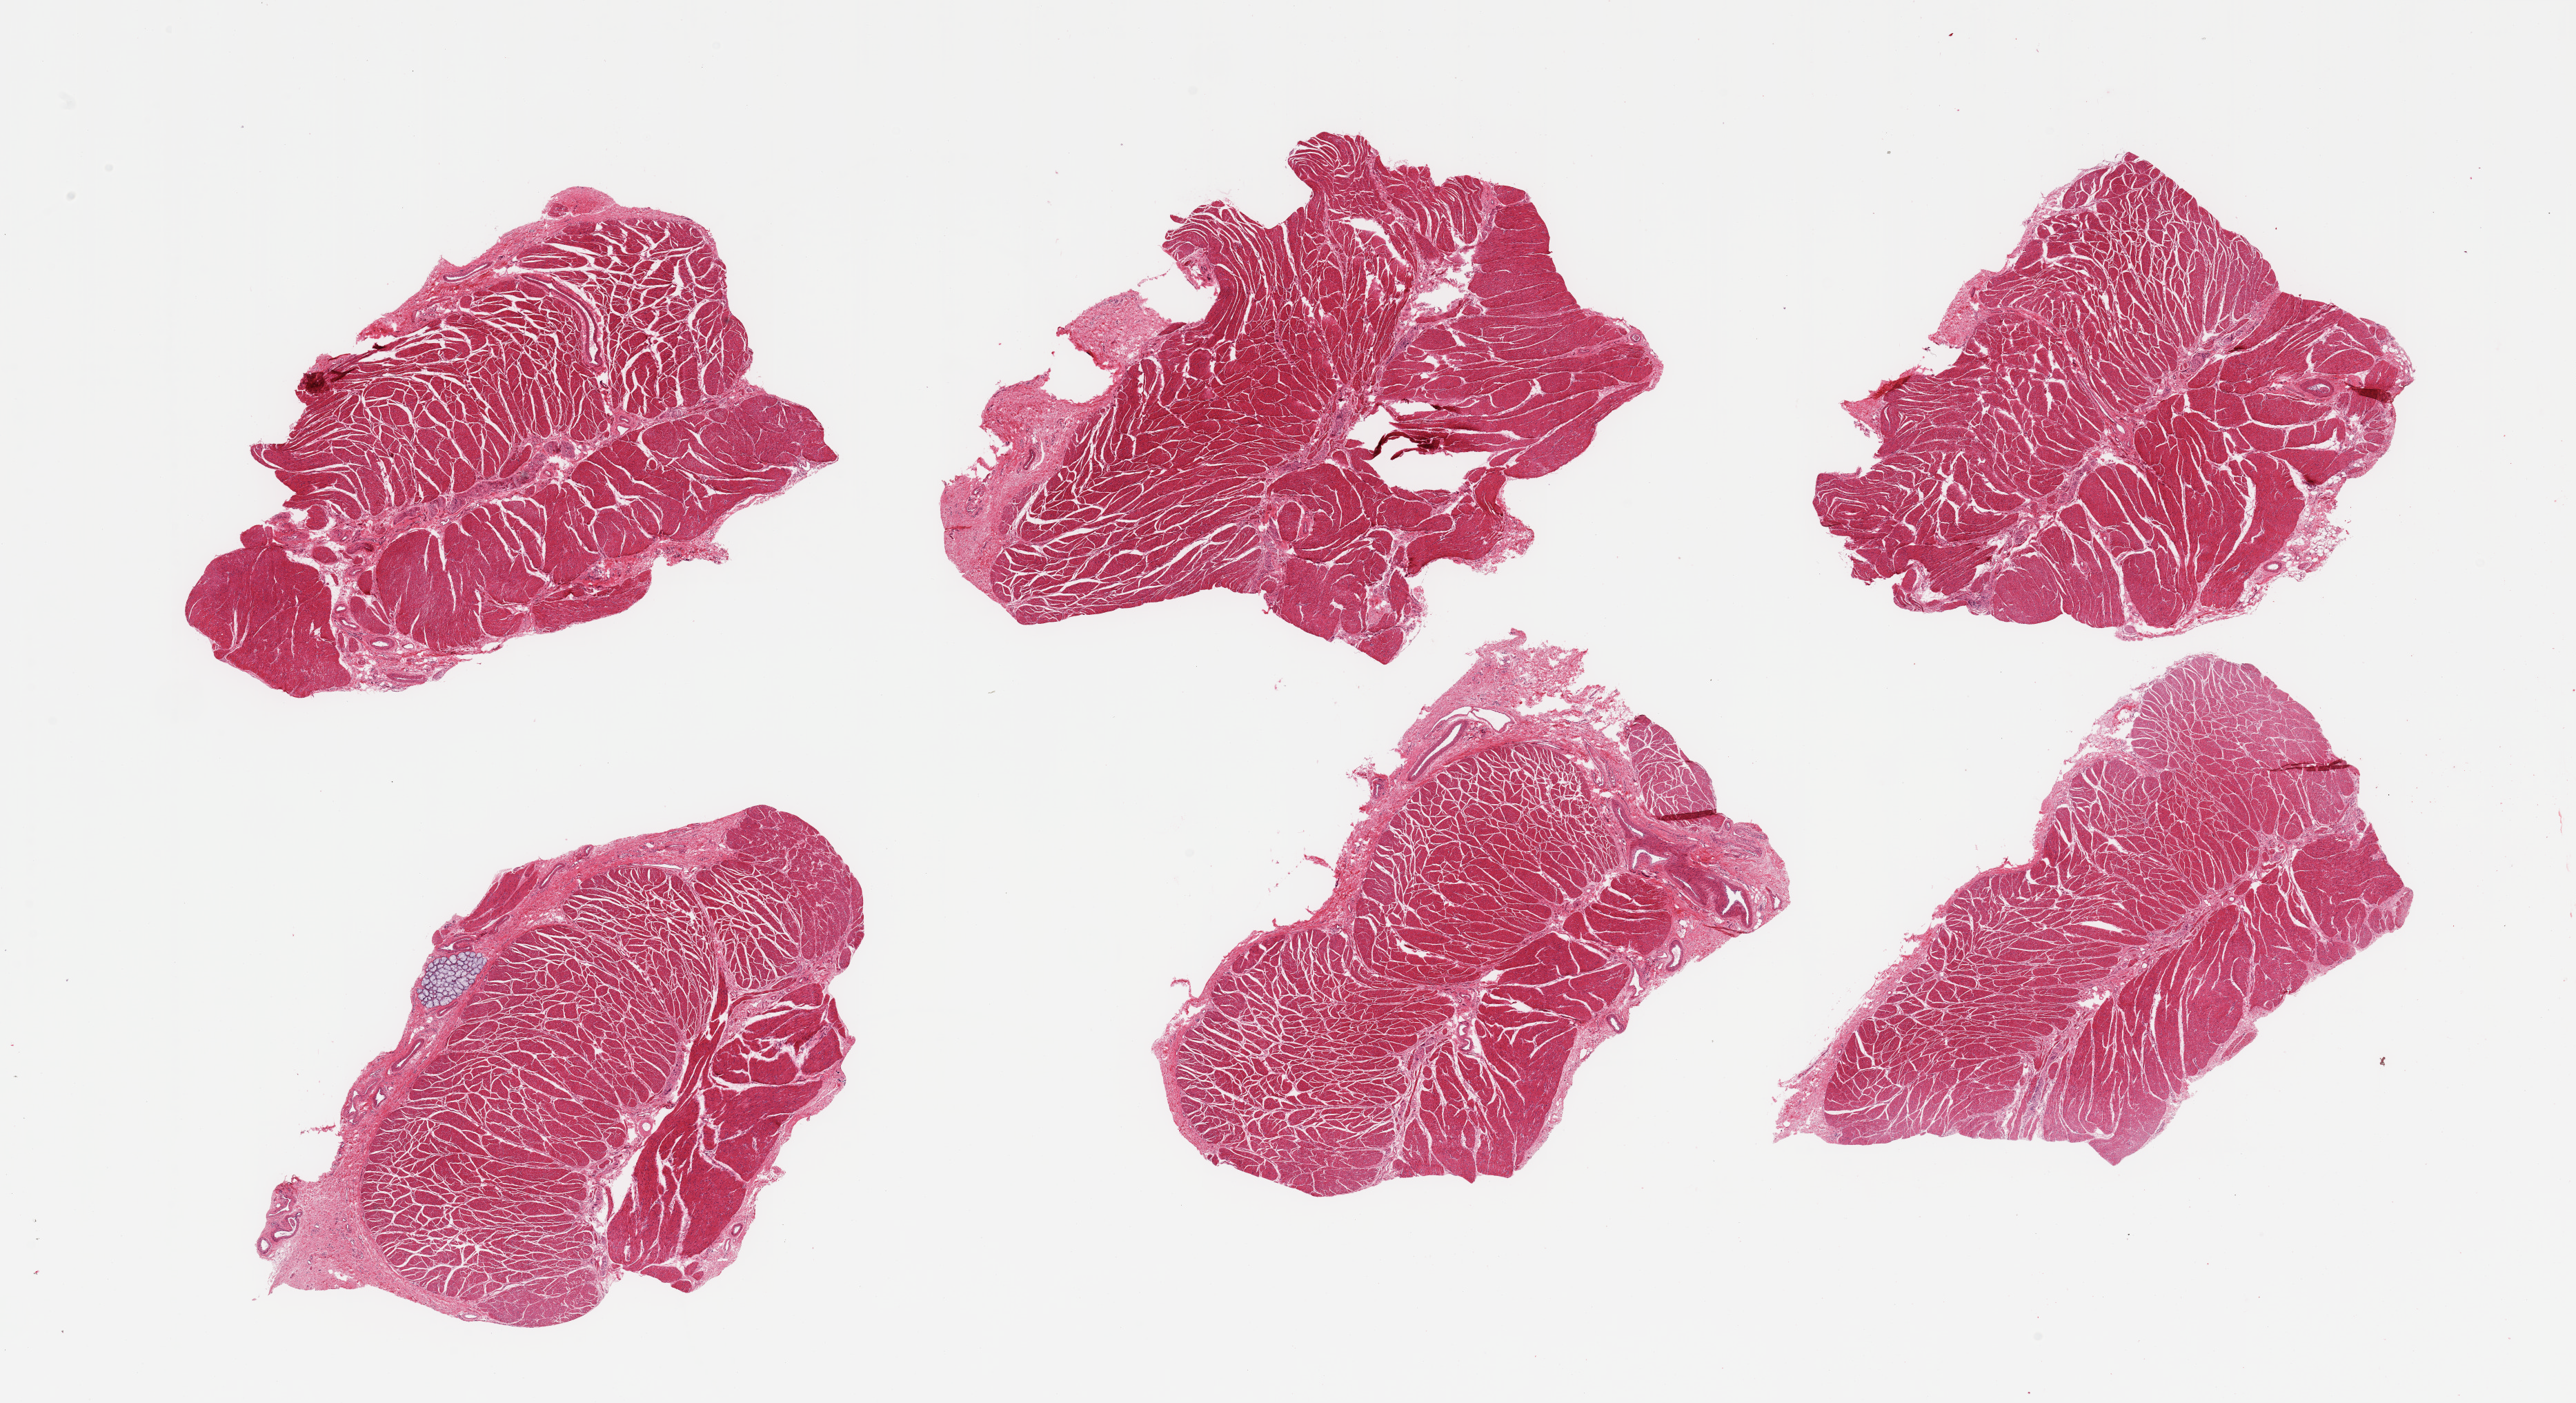
Whole-slide image, H&E stain, brightfield — whole scanned area (about 29.5 x 16.1 mm, from a 20x scan) shown as a low-resolution overview; PAXgene-fixed, paraffin-embedded tissue; section of esophageal muscle (target tissue); tissue donor sample. Donor: male.
• pathologist's review note for this sample: 6 pieces, confirmed target muscularis, single mucus gland